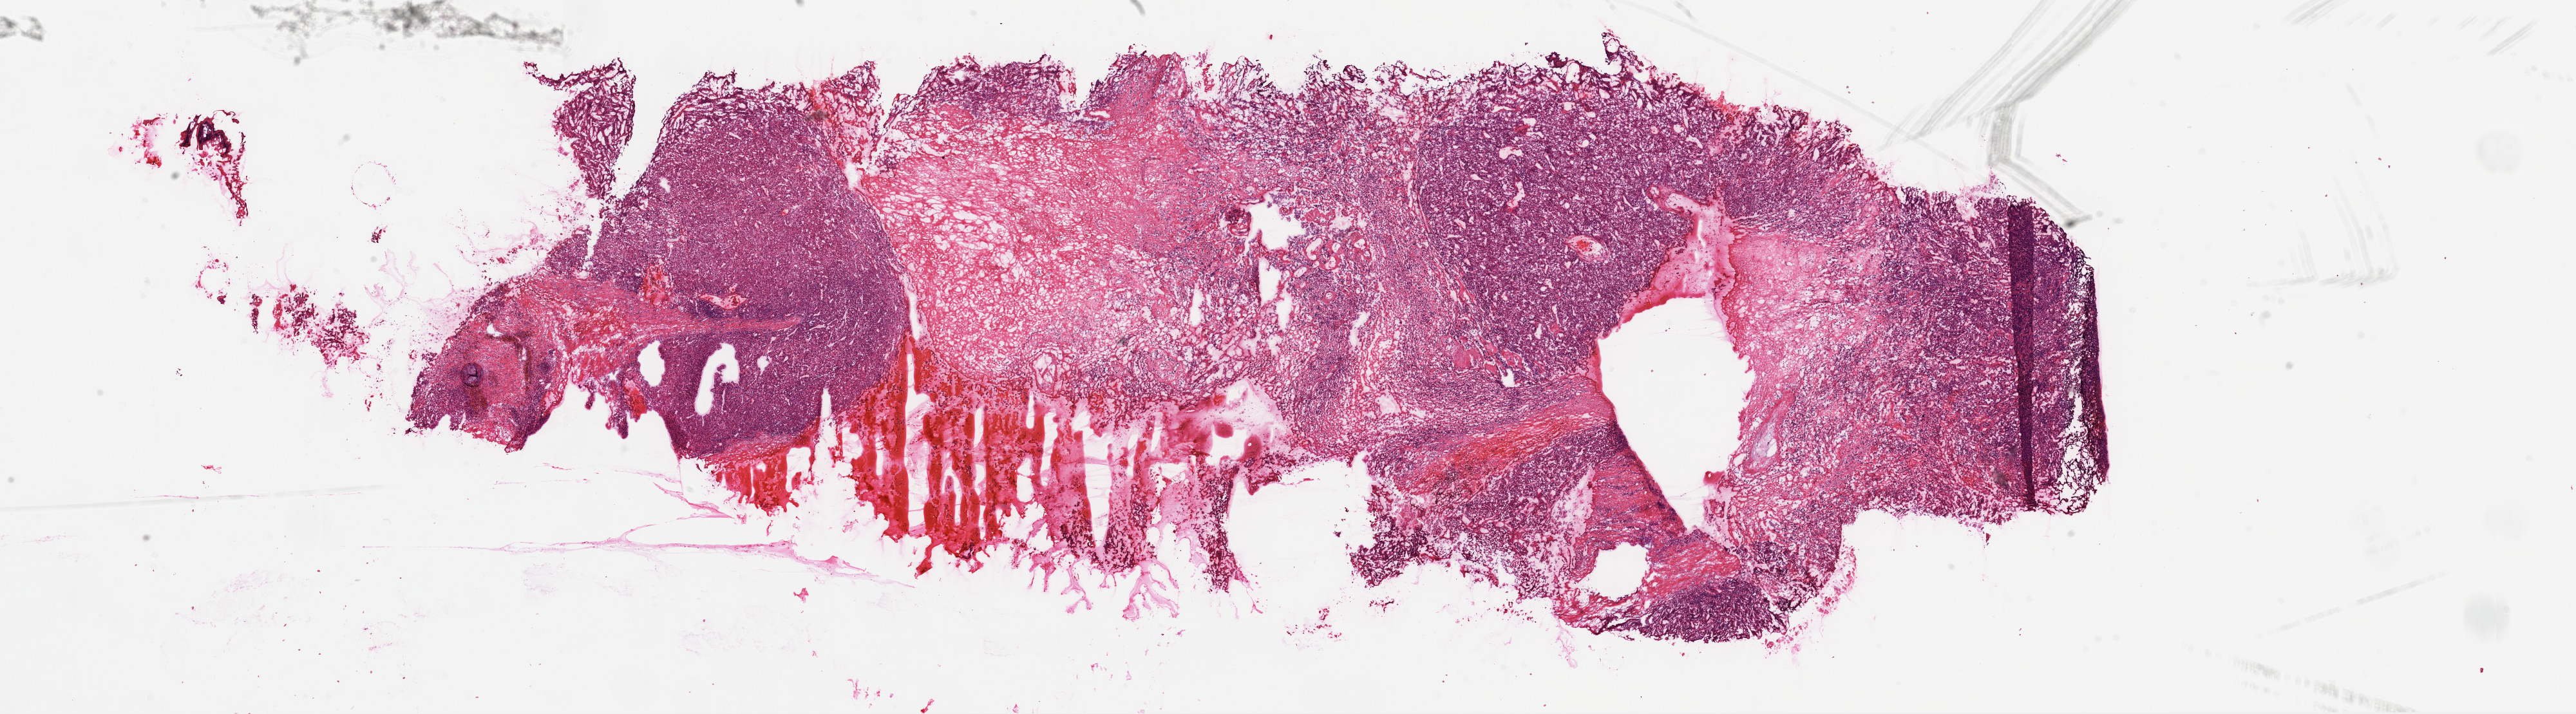
Digitized H&E-stained tissue section (whole slide) — shown as a low-resolution overview of the whole scanned area (about 32.1 x 8.9 mm, from a 20x scan). Frozen section. Primary tumour sample from the kidney. Female patient; age at initial diagnosis 69 years. Histologic grade: G4 (undifferentiated). Slide review estimates, as recorded: tumour cells 65%, tumour nuclei 75%, normal cells 5%, stromal cells 30%, necrosis 0%.
- laterality: left
- pathologic diagnosis: Clear cell adenocarcinoma, NOS
- AJCC pathologic stage: IV
- TNM: T4 N1 M1